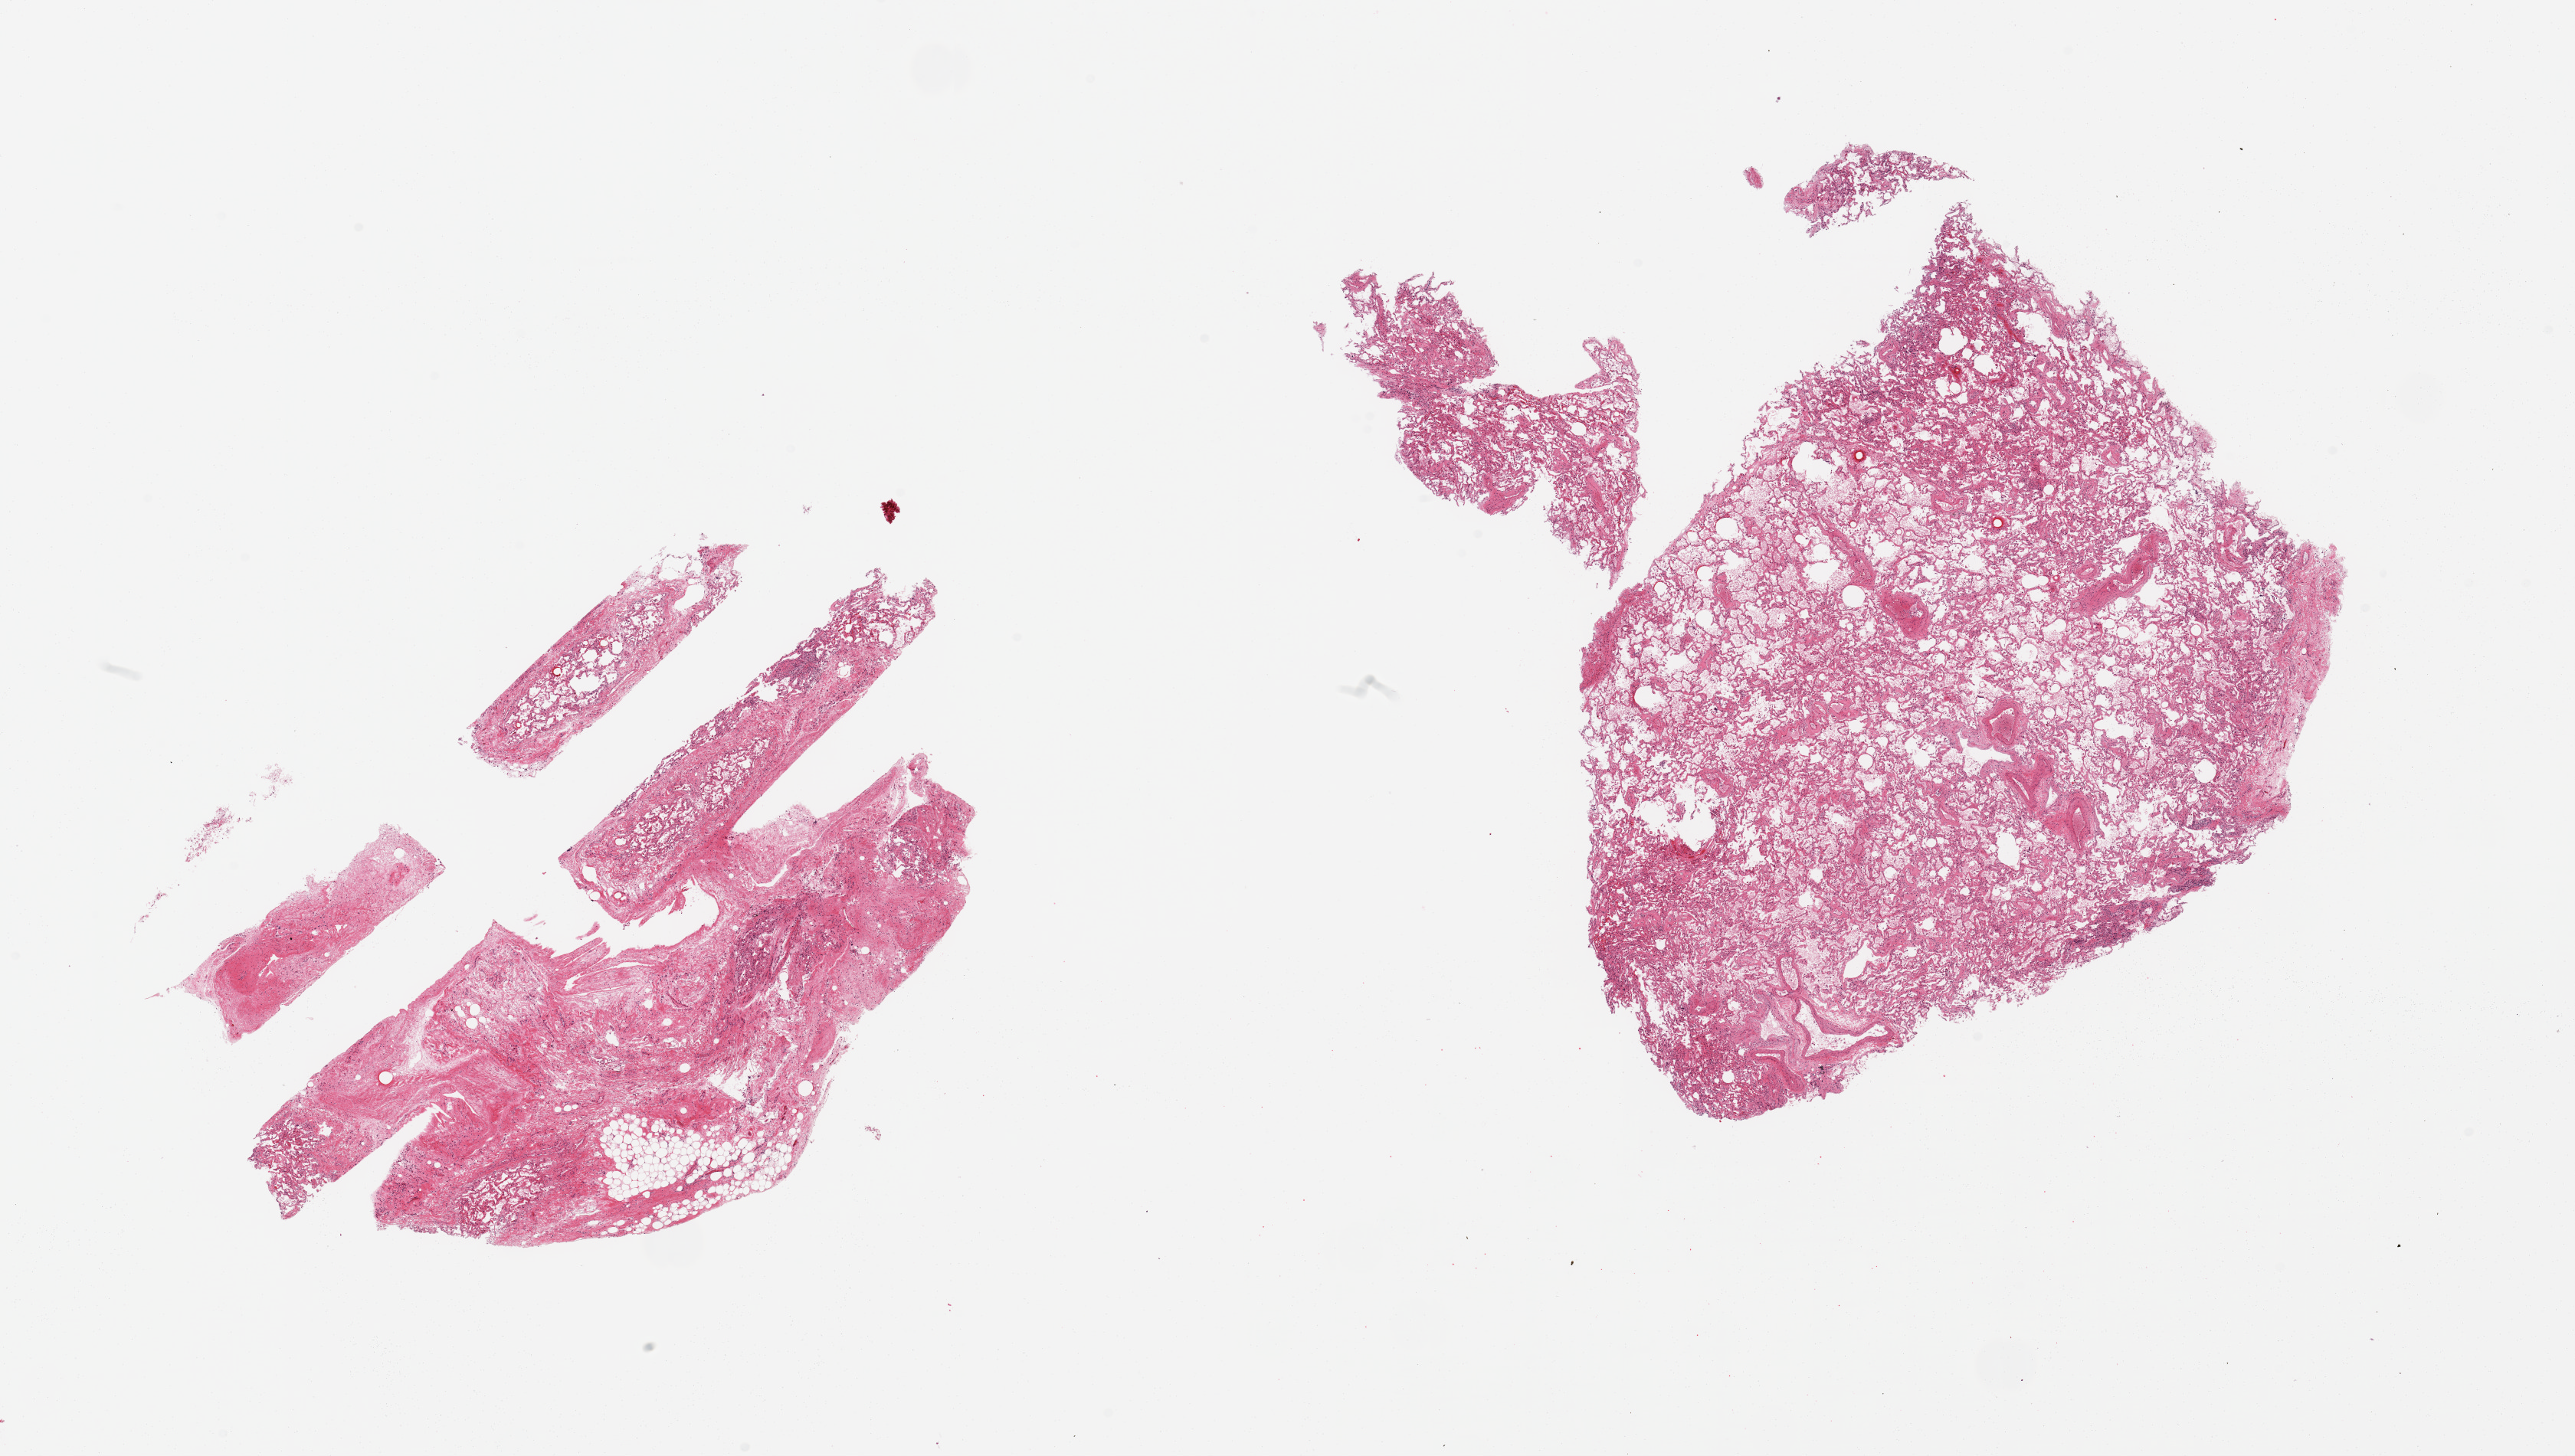
Hematoxylin and eosin (H&E) whole-slide image, a low-resolution overview of the entire scanned area, about 26.6 x 15.0 mm, PAXgene-fixed, paraffin-embedded tissue, sampled site (target tissue): lung, donor tissue sample. Donor sex: male.
- reviewer comment on this tissue sample: 2 pieces, one lung with moderate edema, ~60% of tissue; rest is adherent pleura/fibroadipose tissue; sample carefully